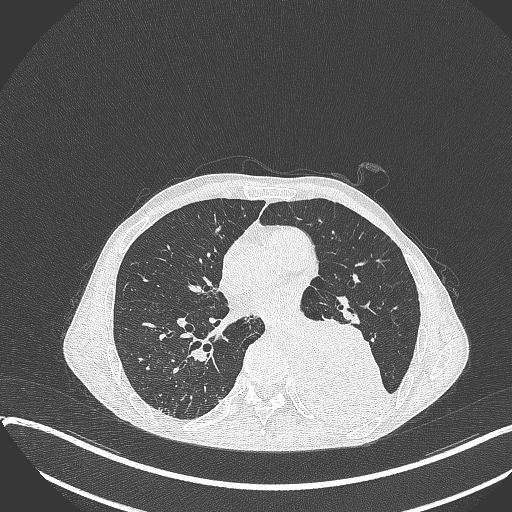
Chest CT, one axial slice. Slice 171 of 401 in the series (ordered by position). Reconstruction kernel B70f. Lung window (W 1500 / L -600 HU). 512 × 512 image matrix, field of view 400 × 400 mm. Male patient, age 57 years. Case-level facts recorded for this patient, not image findings: clinical TNM (as recorded): T4 N0 M0.
Structures marked on this image (bounding box drawn by a radiologist):
- lung tumour (recorded histology: squamous cell carcinoma): box from (x=293, y=307) to (x=393, y=428) px